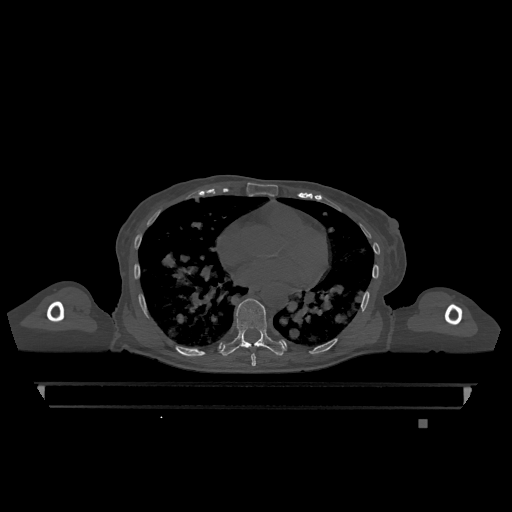
CT including the spine, one axial slice; position 699 of 1317 along the scan axis; bone window (W 1800 / L 400 HU); 0.5 mm slice thickness; 512 × 512 image matrix. Patient: female, 74 years. From the clinical record (not read from this slice): primary cancer: lung; vertebrae with lytic lesions (as recorded): T1, T4, T5, T6, L4, L5.
Annotated regions visible in this slice (semi-automatically segmented with operator editing):
- T7 vertebra: bounding box (x1, y1, x2, y2) in pixels: (251, 353, 256, 367)
- T9 vertebra: (221, 298, 284, 356)